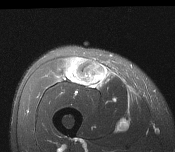
MRI of an extremity soft-tissue mass, one axial slice. Position 61 of 116 along the scan axis. T2-weighted fat-saturated. MR volume resampled by the dataset authors to the PET/CT grid (not the native acquisition matrix). 3.27 mm slice thickness. 175 × 152 image matrix. Male patient. Case-level facts recorded for this patient, not image findings: histological type: pleiomorphic leiomyosarcoma; grade: intermediate; site of the primary tumour: right thigh.
Annotated regions visible in this slice (expert contour drawn on MRI and transferred to this co-registered scan by the dataset authors):
- gross tumour volume including surrounding oedema: bounding box [x1, y1, x2, y2] px = [65, 58, 110, 89]